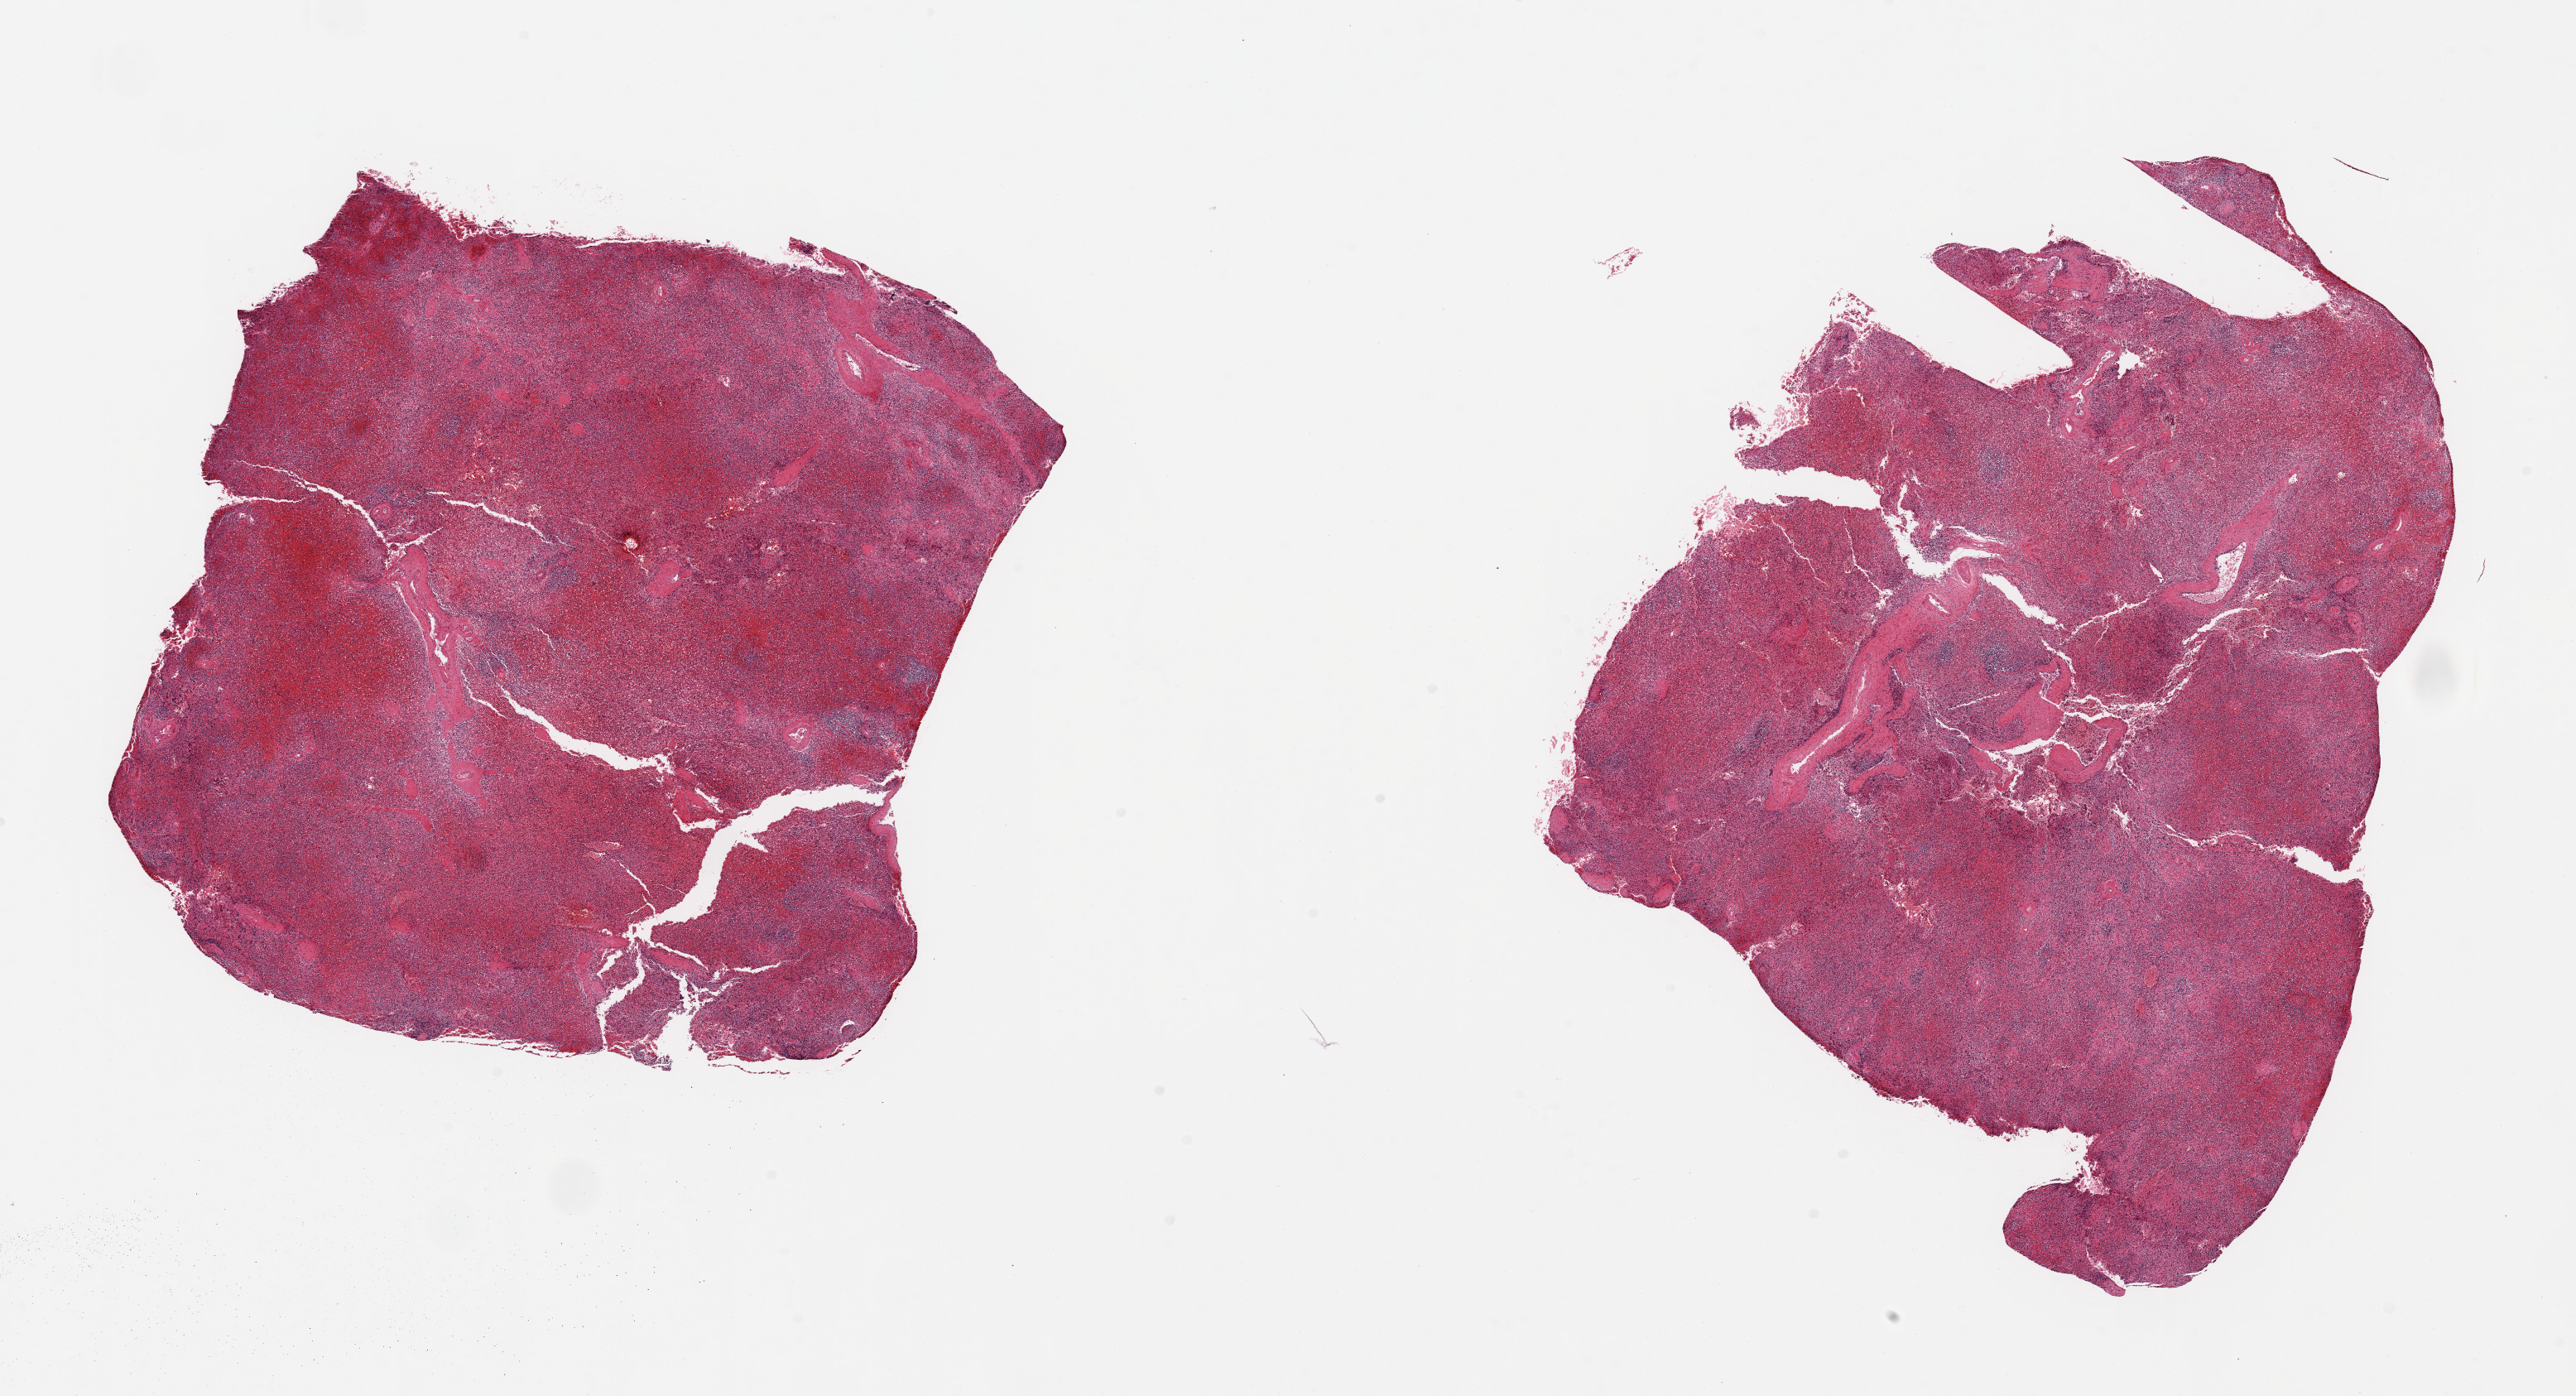
Digitized H&E-stained section — shown as a low-resolution overview of the whole scanned area (about 24.6 x 13.3 mm, from a 20x scan); PAXgene-fixed, paraffin-embedded tissue; section of spleen (target tissue); donor tissue sample. Donor: female.
Pathologist's review note for this sample: 2 pieces, marked congestion.